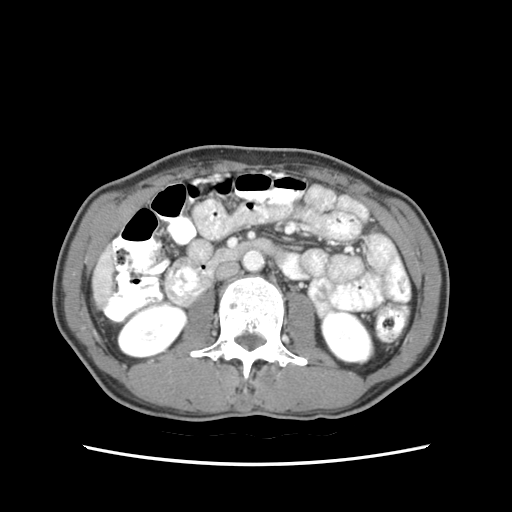
Contrast-enhanced abdominal CT (liver protocol), one axial slice. Soft-tissue window (W 400 / L 40 HU). 512 × 512 image matrix, field of view 320 × 320 mm. From the clinical record (not read from this slice): diagnosis: hepatocellular carcinoma (patient treated with transarterial chemoembolisation; whether this scan precedes or follows treatment is not stated here); TNM stage (as recorded): Stage-IIIB; Child-Pugh class: A; tumour differentiation: moderately differentiated; tumour nodularity: multinodular.
Structures marked on this image (semi-automatically segmented with operator editing):
- liver parenchyma outside the tumour (the mass and vessels are separate outlines, so this box may not span the whole liver): bounding box <94,247,114,306> (left, top, right, bottom; pixels)